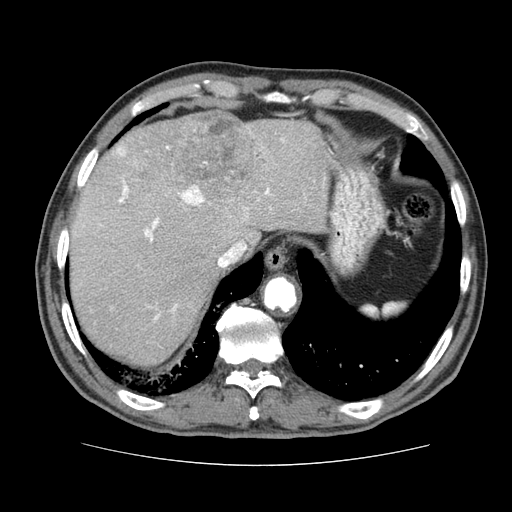
Contrast-enhanced abdominal CT (liver protocol), one axial slice; position 61 of 79 along the scan axis; 120 kVp; soft-tissue window (W 400 / L 40 HU); 512 × 512 image matrix. Case-level facts recorded for this patient, not image findings: diagnosis: hepatocellular carcinoma (patient treated with transarterial chemoembolisation; whether this scan precedes or follows treatment is not stated here); TNM stage (as recorded): Stage-I; Child-Pugh class: A; tumour nodularity: uninodular.
Structures marked on this image (semi-automatically segmented with operator editing):
- liver parenchyma outside the tumour (the mass and vessels are separate outlines, so this box may not span the whole liver): bounding box <68,116,335,366> (left, top, right, bottom; pixels)
- mass: <132,109,264,210>
- liver vessels: <117,139,284,320>